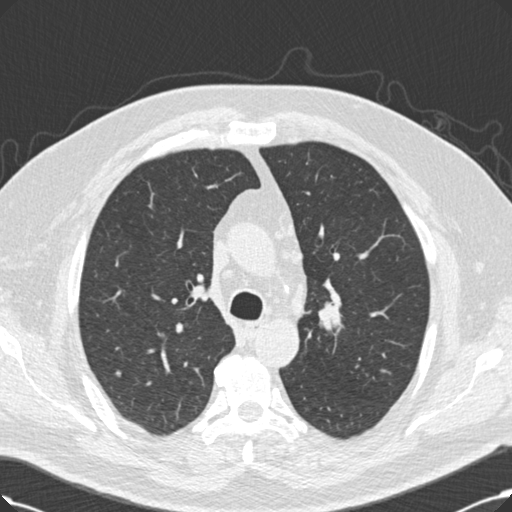
Low-dose screening chest CT, axial slice; third screening round (two years after baseline); lung window (W 1500 / L -600 HU); standard (soft-tissue) reconstruction kernel (B30f); slice 61 of 214 in the series. Male, age 60 years at enrolment.
Expert-annotated lung lesion, bounding box (x1, y1, x2, y2) in pixels: (317, 294, 348, 329). Reader record for this screening exam (exam-level; its link to the box is not recorded): non-calcified nodule or mass ≥4 mm, left upper lobe, 20 × 20 mm, smooth margins, soft tissue attenuation, pre-existing on the prior screen: no. Official screen result: positive, other. Lung cancer was diagnosed 53 days after this screen: squamous cell carcinoma, NOS, right upper lobe, 27 mm at pathology.